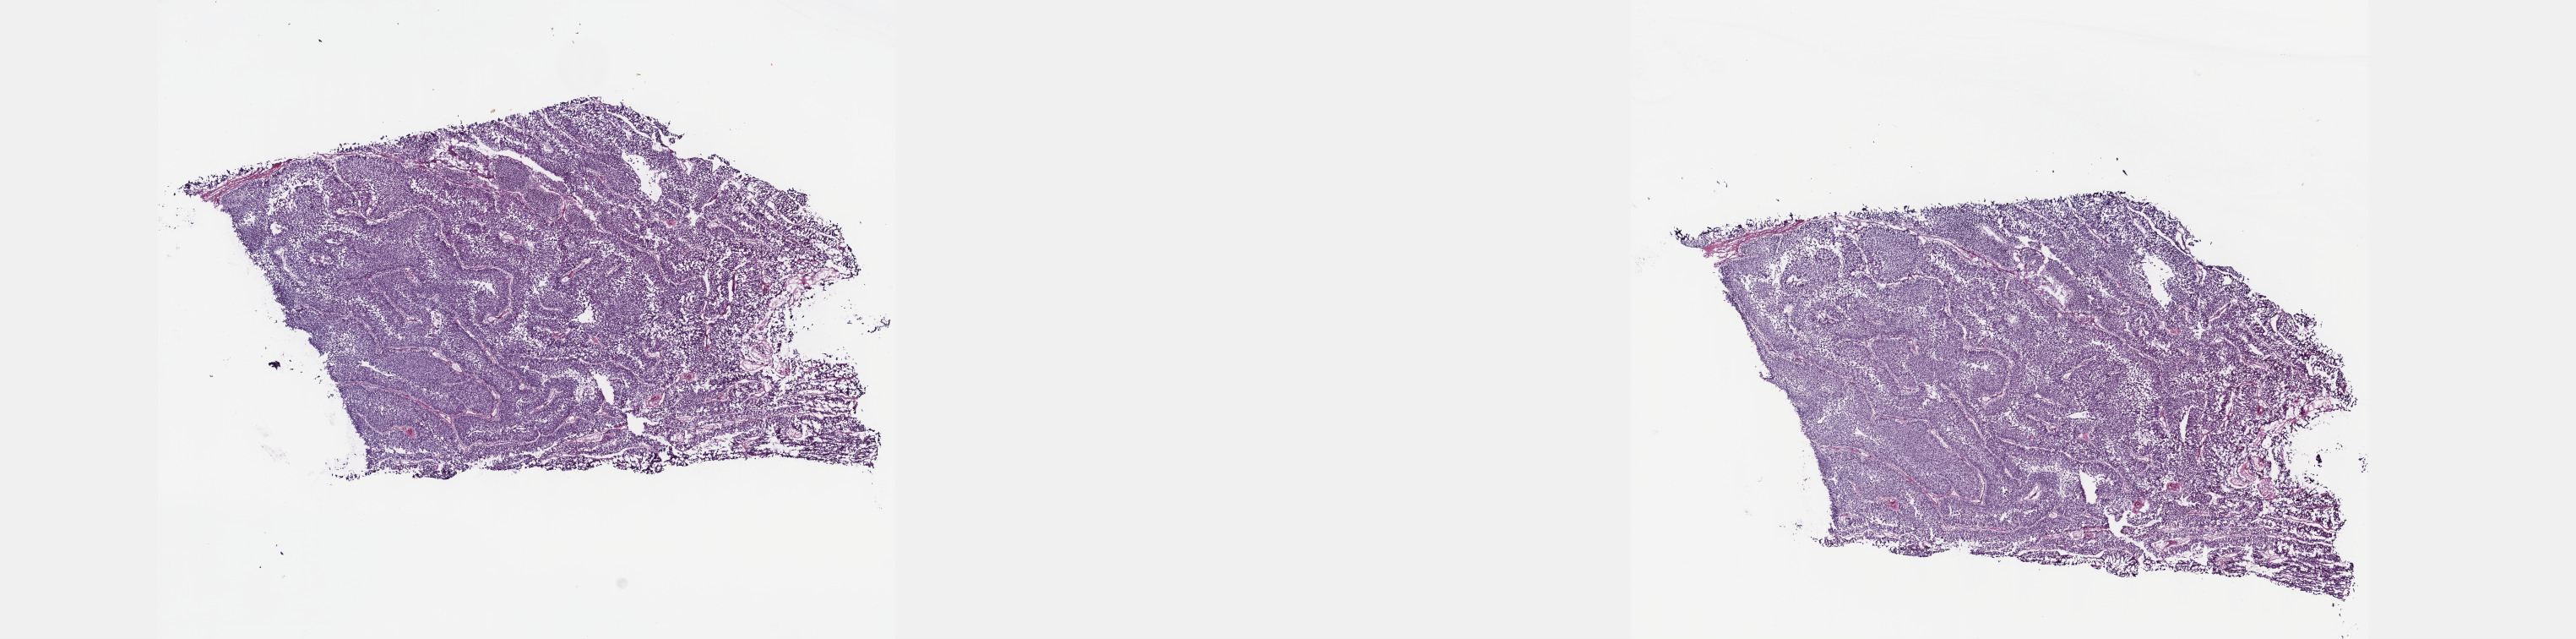
Whole-slide histology image, H&E, whole scanned area (about 24.6 x 6.1 mm, slide scanned at 40x) shown as a low-resolution overview; frozen section; bladder, primary tumour sample. Male, age 50 years at initial diagnosis. Histologic grade: high grade. Slide review estimates, as recorded: tumour cells 100%, tumour nuclei 80%, normal cells 0%, stromal cells 0%, necrosis 0%. Inflammatory infiltration, as recorded: lymphocyte infiltration 2%, monocyte infiltration 0%, neutrophil infiltration 0%.
• histologic diagnosis: Papillary transitional cell carcinoma
• AJCC pathologic stage: I